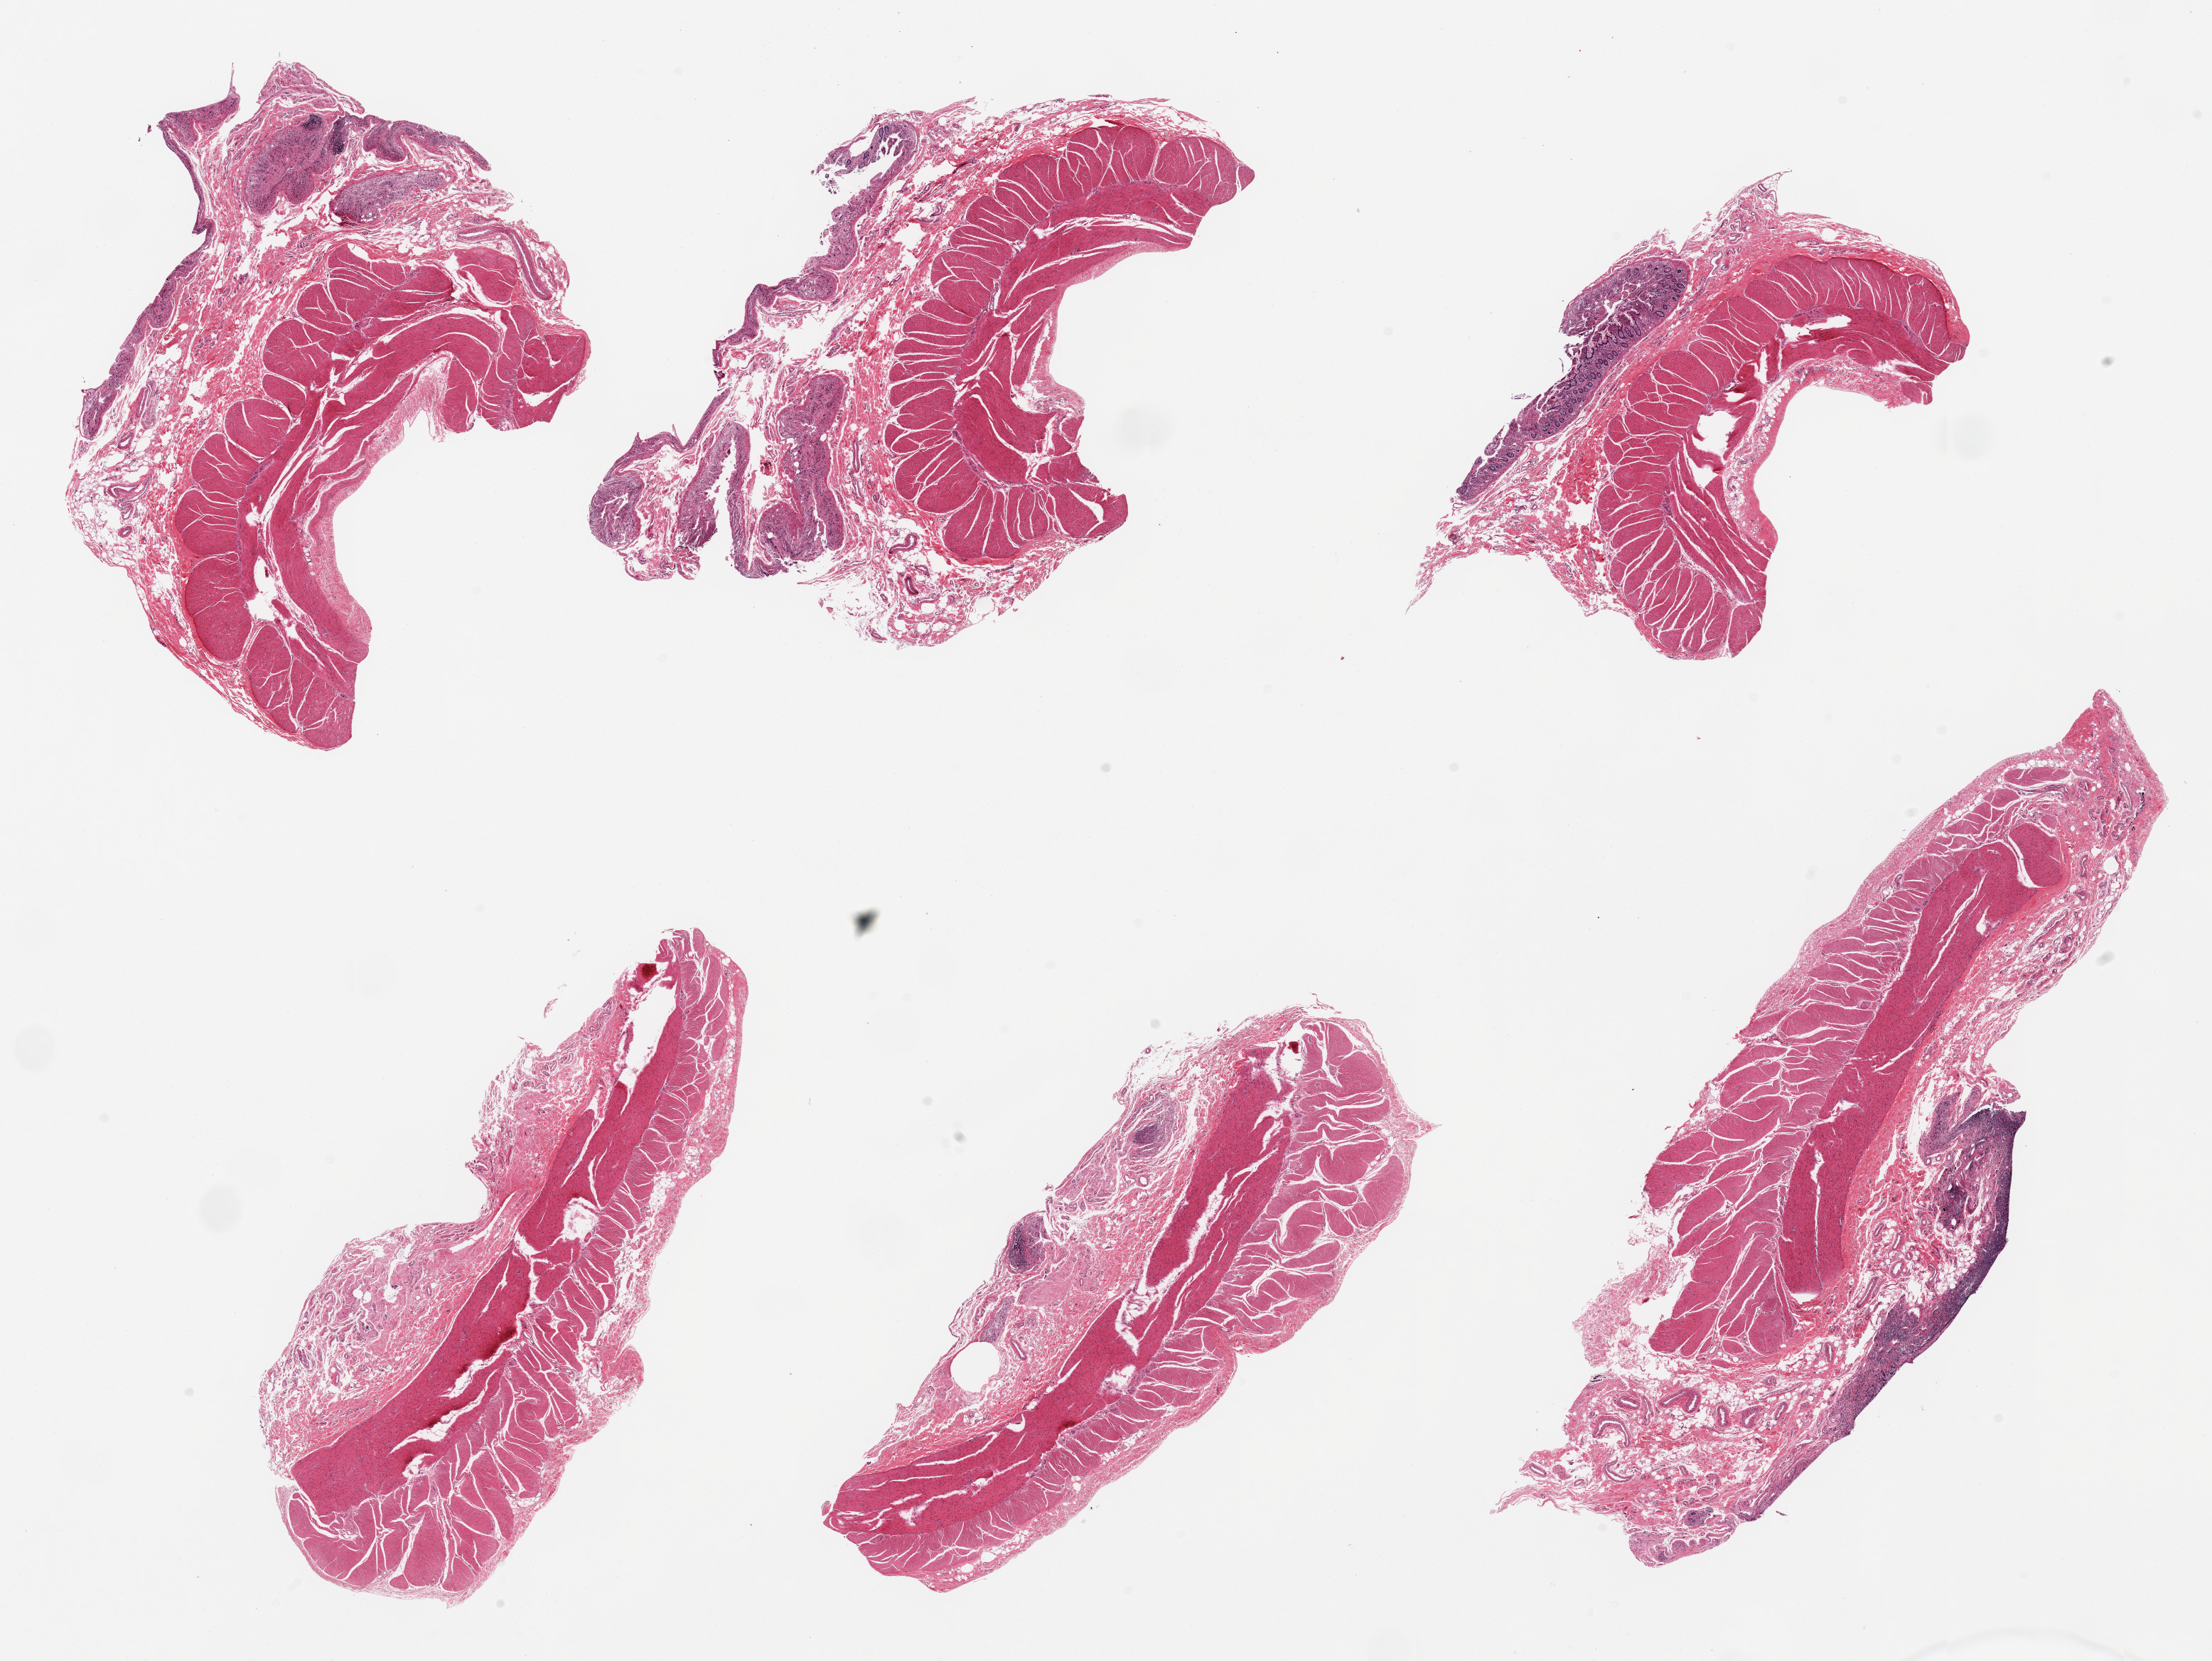
Digitized hematoxylin and eosin (H&E)-stained section, a low-resolution overview of the entire scanned area, about 24.6 x 18.5 mm, PAXgene-fixed paraffin-embedded (PFPE) section, section of ileum (target tissue), tissue donor sample. Donor: male.
* review note (as recorded): 6 pieces; predominantly muscularis (not target) with autolyzed mucosa and only focal lymphoid elements